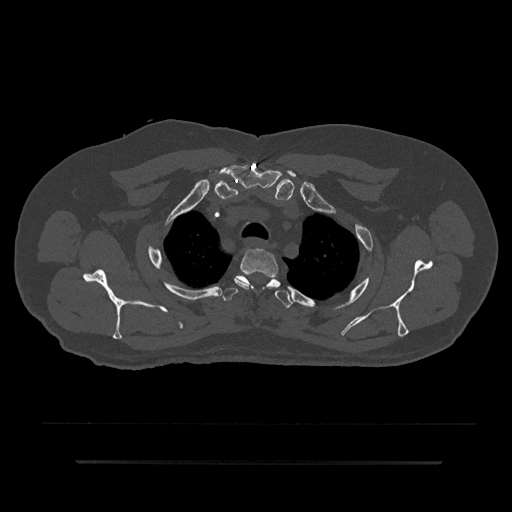
CT including the spine, one axial slice; slice 681 of 797 in the series (ordered by position); reconstruction kernel Br40s/3; bone window (W 1800 / L 400 HU); 512 × 512 image matrix, field of view 464 × 464 mm. Male patient, age 59 years. Case-level facts recorded for this patient, not image findings: primary cancer: bile ducts; vertebrae with lytic lesions (as recorded): T10.
Structures marked on this image (semi-automatically segmented with operator editing):
- T2 vertebra: bounding box (x1, y1, x2, y2) in pixels: (234, 249, 279, 291)
- T3 vertebra: (223, 275, 293, 308)